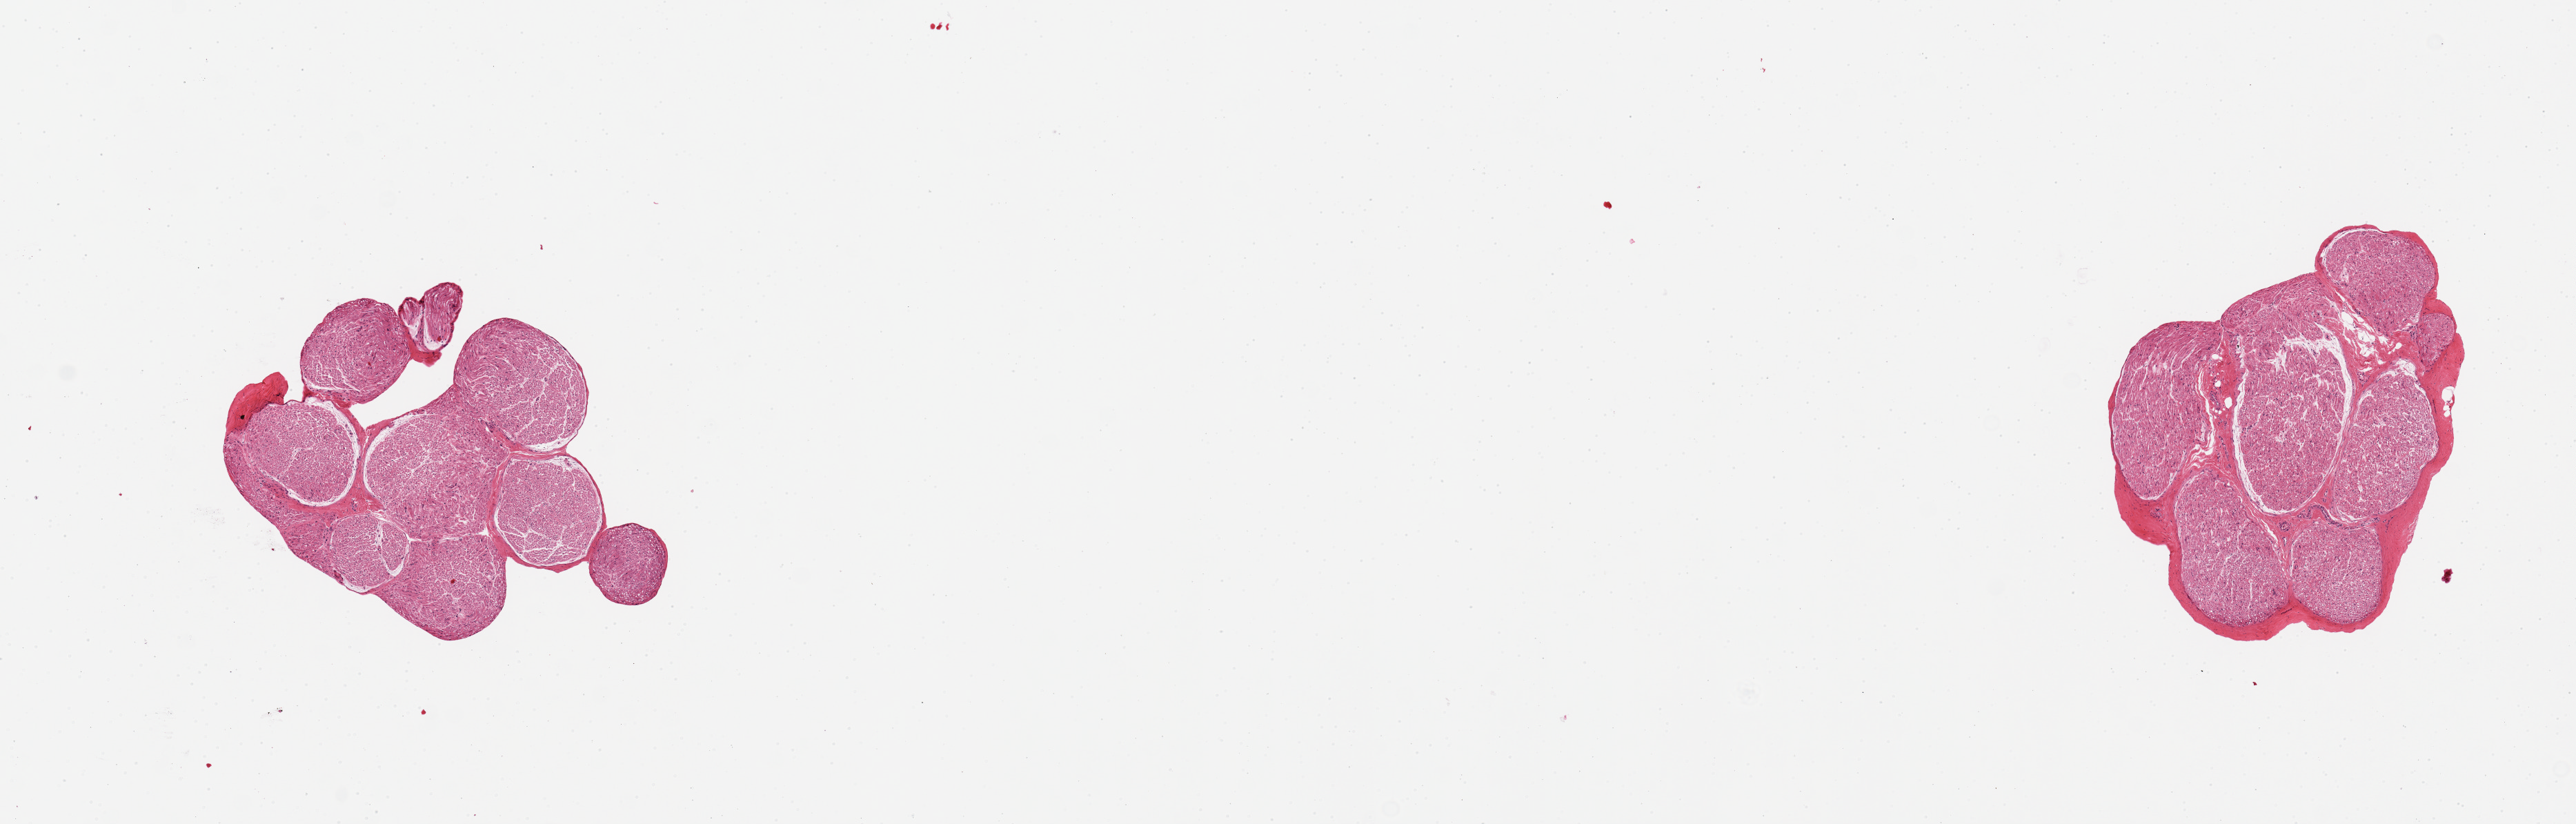
Whole-slide image, hematoxylin and eosin (H&E) stain, whole scanned area (about 14.8 x 4.7 mm) shown as a low-resolution overview; PAXgene-fixed, paraffin-embedded tissue; target tissue: tibial nerve; tissue donor sample. Donor: female.
Reviewer comment on this tissue sample: 2 pieces, well trimmed.